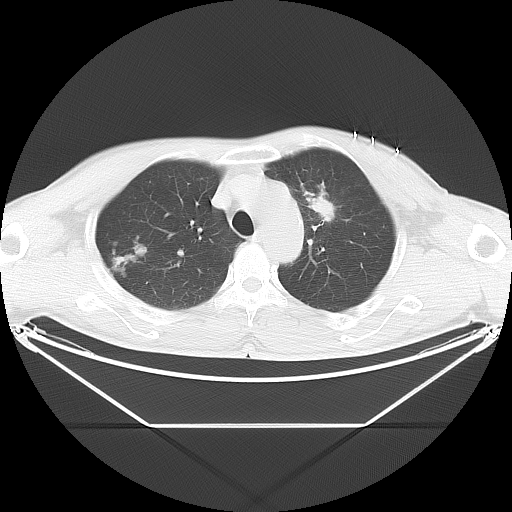
Chest CT, one axial slice. Position 20 of 28 along the scan axis. 120 kVp. Lung window (W 1500 / L -600 HU). 5 mm slice thickness. 512 × 512 image matrix, field of view 443 × 443 mm. Male patient, age 60 years. Case-level facts recorded for this patient, not image findings: clinical TNM (as recorded): T2 N1 M0.
Structures marked on this image (rectangle marked by the reading radiologist):
- lung tumour (recorded histology: adenocarcinoma): box from (x=309, y=198) to (x=337, y=224) px